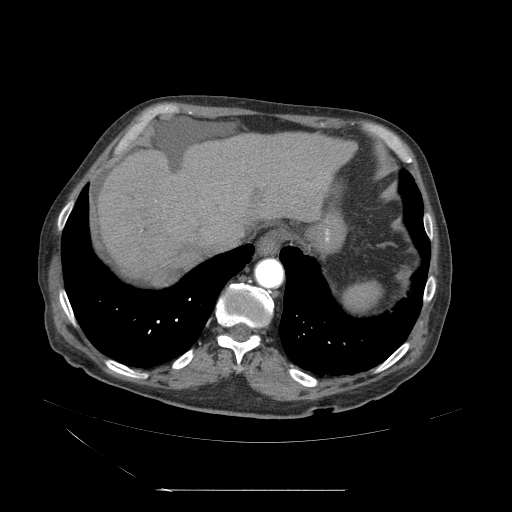
Contrast-enhanced abdominal CT (liver protocol), one axial slice. 120 kVp. Soft-tissue window (W 400 / L 40 HU). 512 × 512 image matrix, field of view 440 × 440 mm. From the clinical record (not read from this slice): diagnosis: hepatocellular carcinoma (patient treated with transarterial chemoembolisation; whether this scan precedes or follows treatment is not stated here); TNM stage (as recorded): Stage-II; Child-Pugh class: A; tumour nodularity: multinodular; tumour size: 1 cm.
Annotated regions visible in this slice (semi-automatically segmented with operator editing):
- abdominal aorta: box from (x=254, y=258) to (x=284, y=288) px
- liver parenchyma outside the tumour (the mass and vessels are separate outlines, so this box may not span the whole liver): (x=98, y=133)–(x=347, y=284)
- mass: (x=147, y=272)–(x=181, y=296)
- liver vessels: (x=100, y=196)–(x=240, y=260)